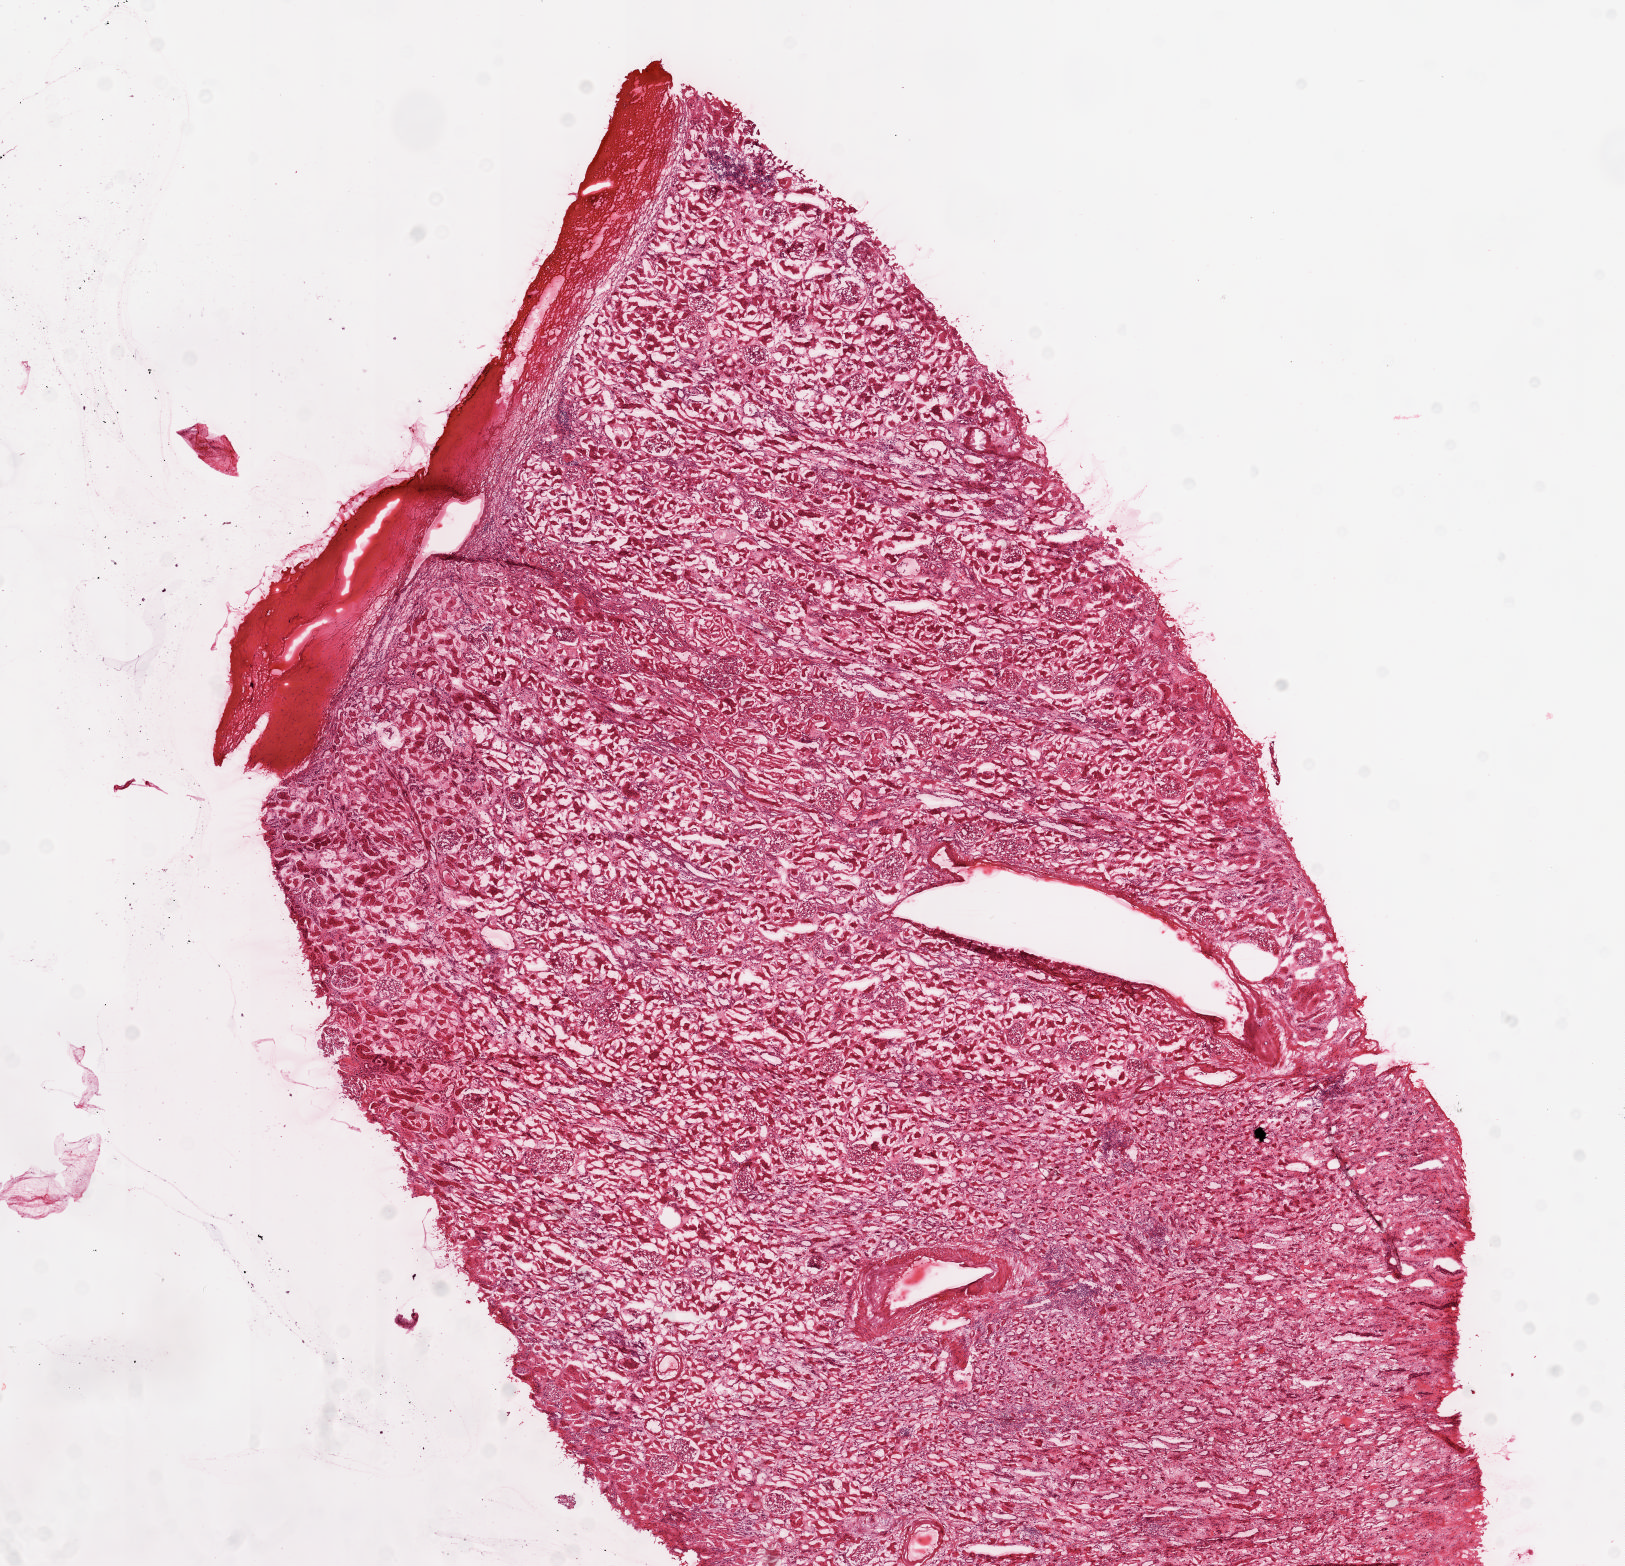
H&E-stained whole-slide image, whole scanned area (about 12.9 x 12.4 mm) shown as a low-resolution overview; frozen section from the top of the tissue portion; kidney, solid tissue normal (non-tumour tissue) sample. Female, age 72 years at initial diagnosis.
This section: solid tissue normal (non-tumour) sample from the same patient. Patient diagnosis: Clear cell adenocarcinoma, NOS.